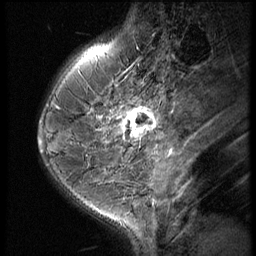
Breast MRI (dynamic contrast-enhanced), one sagittal slice. Slice 20 of 60 in the series (ordered by position). 3 images stored at this slice position (order not interpretable as contrast timing). 1.5 T. TE 4.2 ms, TR 9 ms. 2.5 mm slice thickness. 256 × 256 image matrix, field of view 180 × 180 mm. Patient: female, 38 years. From the clinical record (not read from this slice): setting: breast cancer imaged before/during neoadjuvant chemotherapy; receptor status: triple-negative.
Annotated regions visible in this slice (semi-automatically segmented with operator editing):
- analysis volume of interest (the breast-tissue region the enhancement analysis was run in; not a lesion): bounding box (x1, y1, x2, y2) in pixels: (119, 93, 165, 150)
- tumour enhancement mask (voxels above the 140 % enhancement threshold inside the analysis volume of interest): (119, 107, 159, 140)